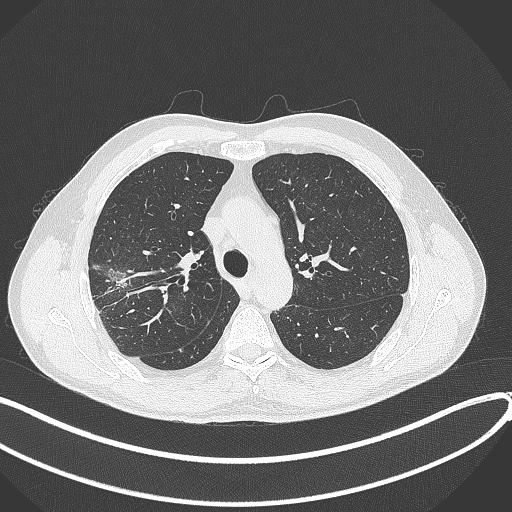
Chest CT, one axial slice; position 297 of 381 along the scan axis; lung window (W 1500 / L -600 HU); 512 × 512 image matrix, field of view 400 × 400 mm. Patient: male, 62 years. Case-level facts recorded for this patient, not image findings: clinical TNM (as recorded): T1c N0 M0; histopathological grade: G2-3.
Annotated regions visible in this slice (rectangle marked by the reading radiologist):
- lung tumour (recorded histology: adenocarcinoma): box from (x=105, y=268) to (x=129, y=289) px